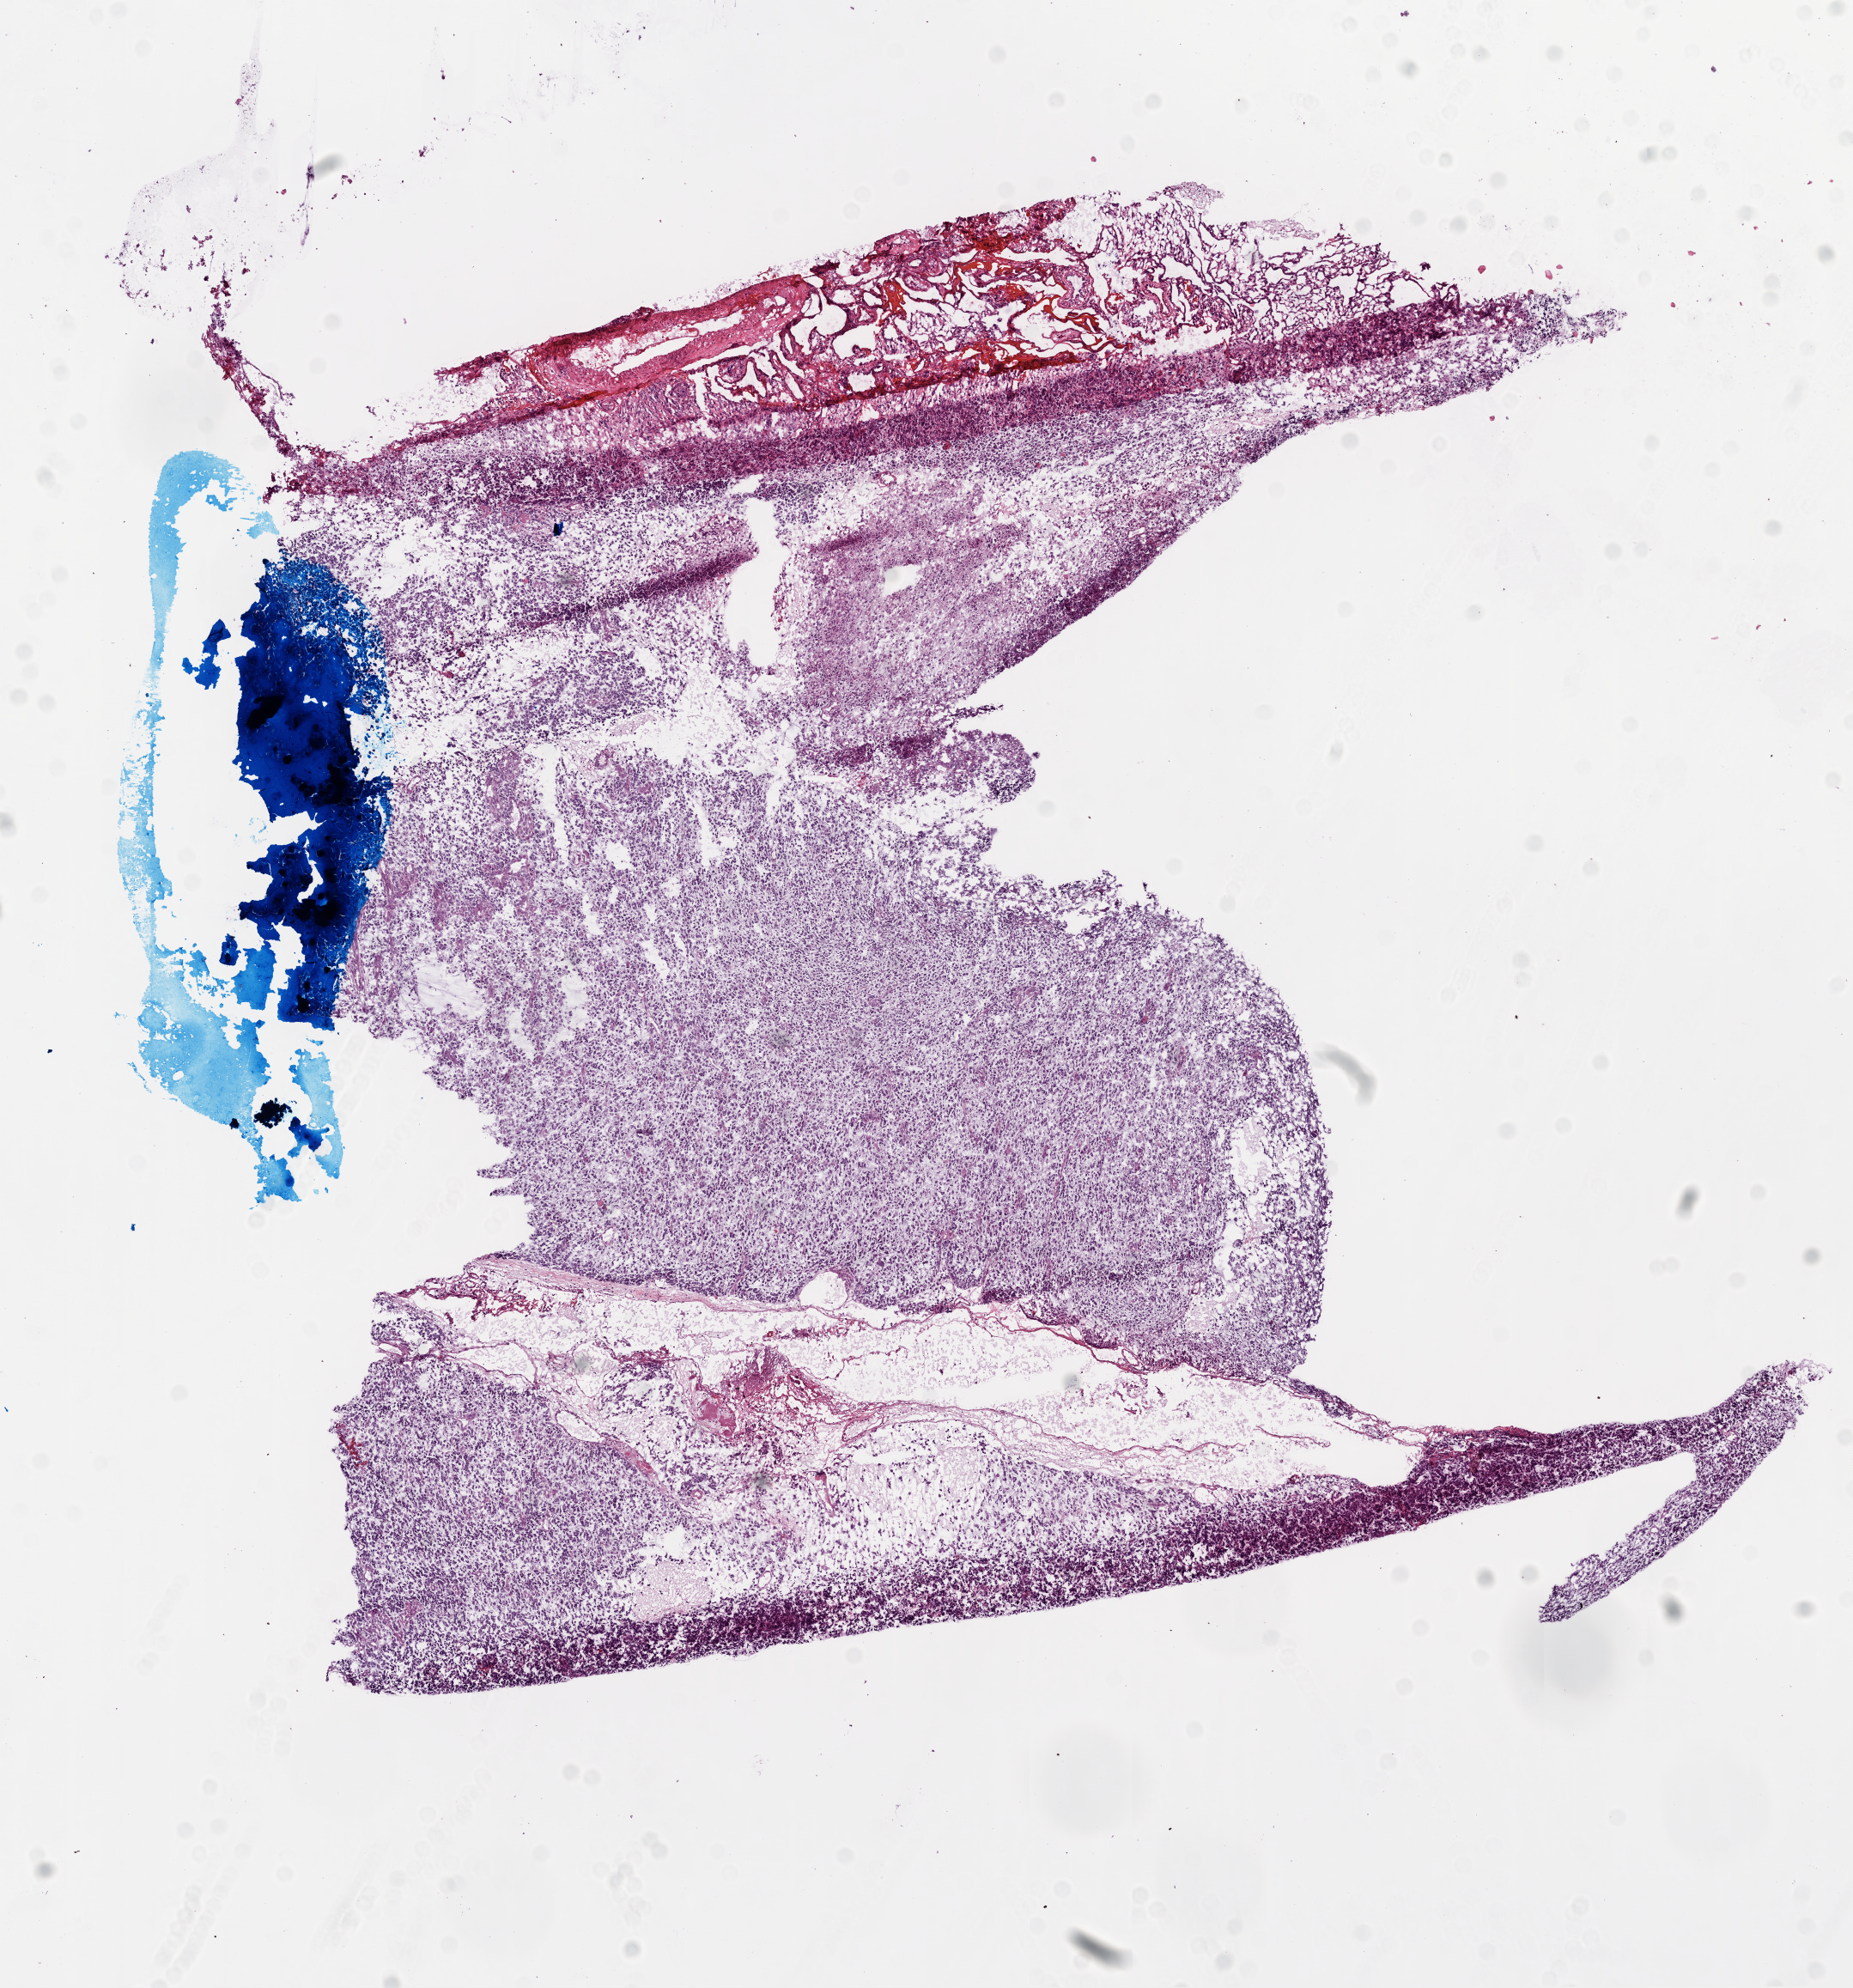
Digitized H&E tissue section (whole slide) — shown as a low-resolution overview of the whole scanned area (about 8.7 x 9.3 mm); frozen section; sample: primary tumour, brain. Female, age 17 years at initial diagnosis. Slide review estimates, as recorded: tumour cells 85%, tumour nuclei 90%, normal cells 0%, stromal cells 5%, necrosis 10%.
Histologic diagnosis: Glioblastoma.